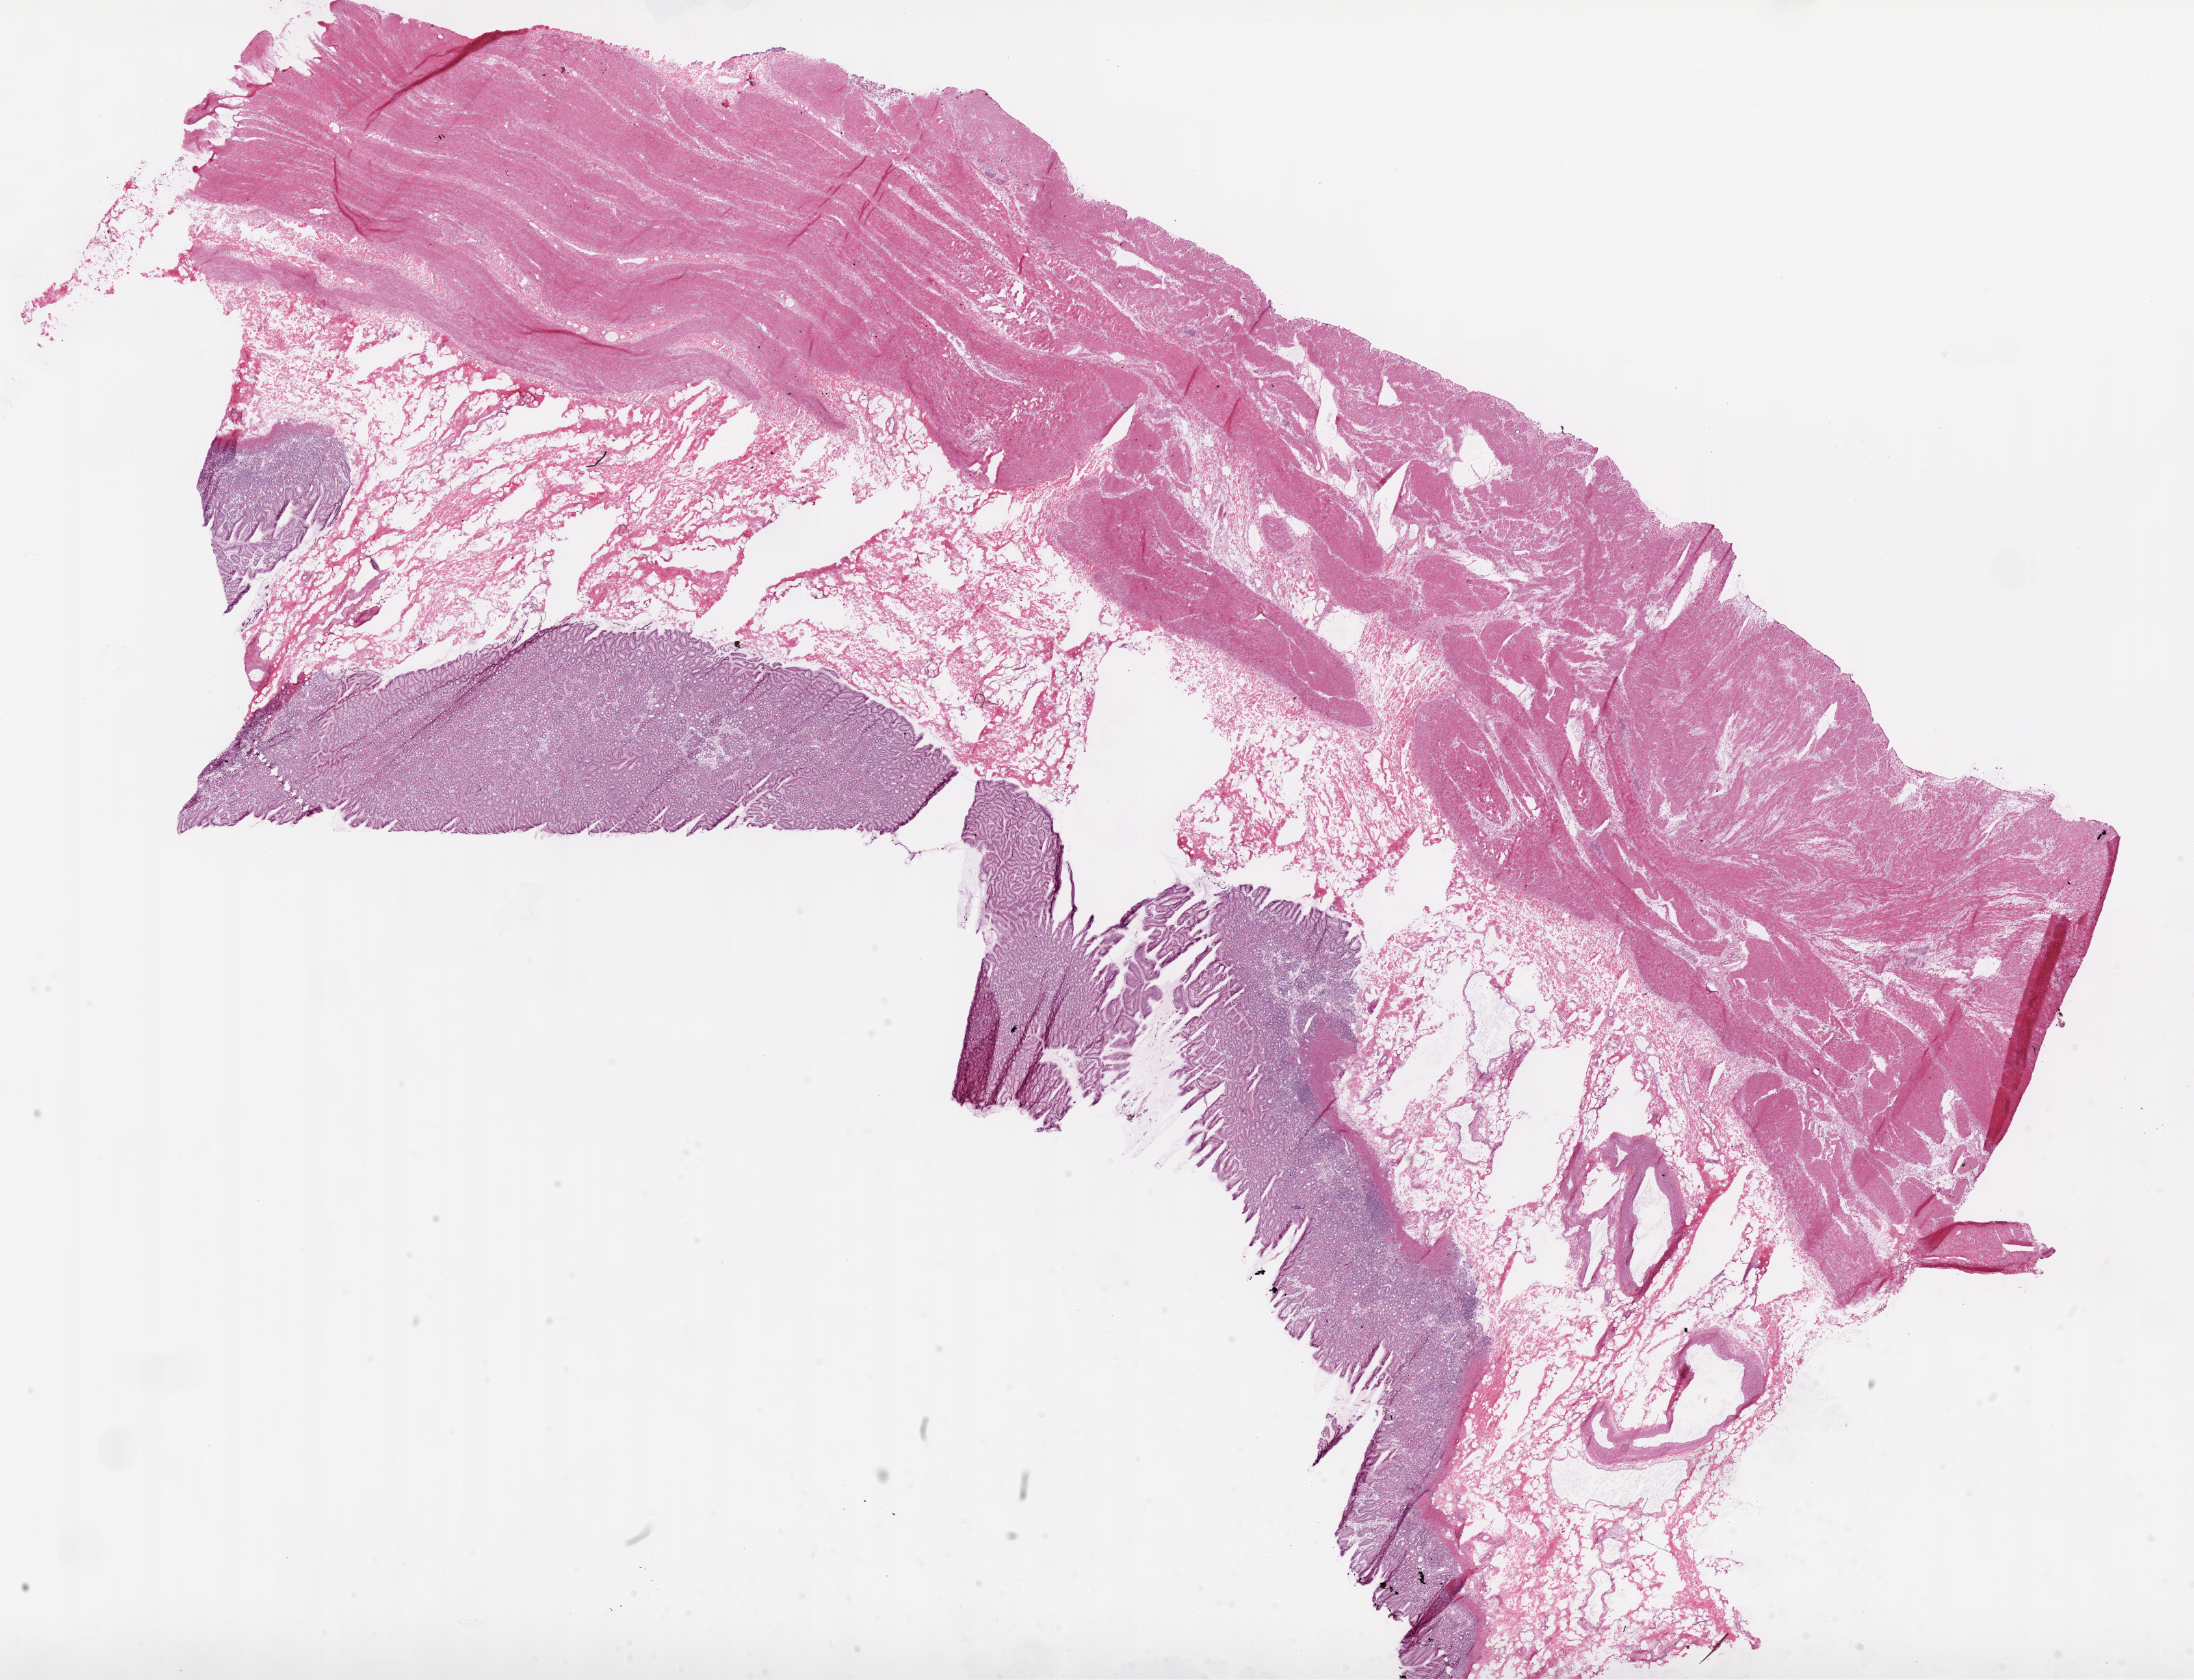
Whole-slide histology image, H&E-stained — low-resolution overview of the scanned area, about 27.1 x 20.7 mm. Frozen section. Stomach, solid tissue normal (non-tumour tissue) sample. Male patient; age at initial diagnosis 80 years.
This section: solid tissue normal (non-tumour) sample from the same patient. Patient diagnosis: Adenocarcinoma, NOS (gastric antrum).